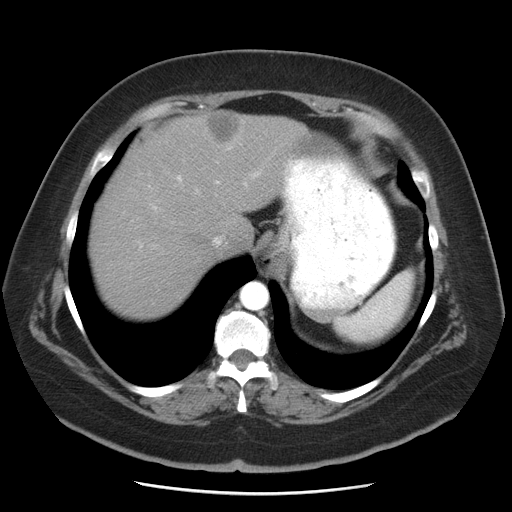
Contrast-enhanced abdominal CT, one axial slice; slice 39 of 55 in the series (ordered by position); 120 kVp; intravenous contrast given; soft-tissue window (W 400 / L 40 HU); 5 mm slice thickness; 512 × 512 image matrix. Female patient, age 52 years. Case-level facts recorded for this patient, not image findings: diagnosis: colorectal cancer liver metastases, imaged before liver resection; multiple liver metastases: yes; largest metastasis: 2.5 cm; disease in both lobes: yes.
Annotated regions visible in this slice (outlined manually by an expert reader):
- hepatic veins: bounding box (x1, y1, x2, y2) in pixels: (213, 237, 222, 245)
- liver: (88, 111, 309, 321)
- planned liver remnant (the part of the liver to remain after resection): (88, 162, 206, 321)
- portal vein (with intrahepatic branches): (153, 144, 262, 209)
- liver metastasis: (204, 112, 243, 144)